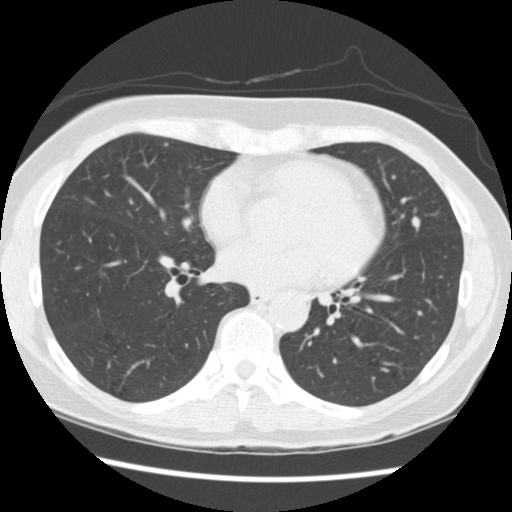
Low-dose screening chest CT, axial slice; third annual screen; lung window (W 1500 / L -600 HU); 2.5 mm slice thickness; slice 141 of 262 in the series. Female participant, aged 60 years at enrolment. Current smoker at enrolment.
Expert-annotated lung lesion, bounding box <393,206,435,247> (left, top, right, bottom; pixels). Screening reader's record for this exam (one nodule recorded; not confirmed to be the boxed lesion): non-calcified nodule or mass ≥4 mm, lingula, 6 × 5 mm, smooth margins, soft tissue attenuation, pre-existing on the prior screen: yes; interval growth: yes. Official screen result: positive, other. Lung cancer was diagnosed 209 days after this screen: adenocarcinoma, NOS, lingula, poorly differentiated (G3), stage IA (AJCC 6th edition), 6 mm at pathology.